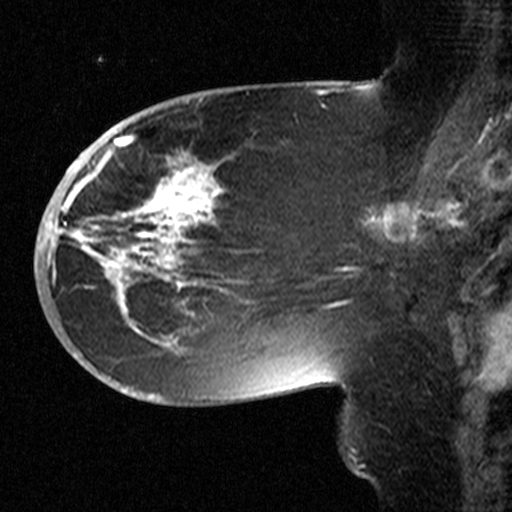
Breast MRI (dynamic contrast-enhanced), one sagittal slice; slice 19 of 44 in the series (ordered by position); dynamic contrast-enhanced study with each time point stored as its own series, time point 2 of 3 at this slice position (early post-contrast, ordered by acquisition time); 1.5 T; TE 4.5 ms, TR 11 ms; 512 × 512 image matrix, field of view 200 × 200 mm. Patient: female, 53 years. Case-level facts recorded for this patient, not image findings: setting: breast cancer imaged before/during neoadjuvant chemotherapy; receptor status: HR-positive, HER2-negative.
Structures marked on this image (semi-automatic segmentation, software-assisted and operator-edited):
- analysis volume of interest (the breast-tissue region the enhancement analysis was run in; not a lesion): box from (x=58, y=154) to (x=311, y=367) px
- tumour enhancement mask (voxels above the 90 % enhancement threshold inside the analysis volume of interest): (x=60, y=154)–(x=223, y=345)